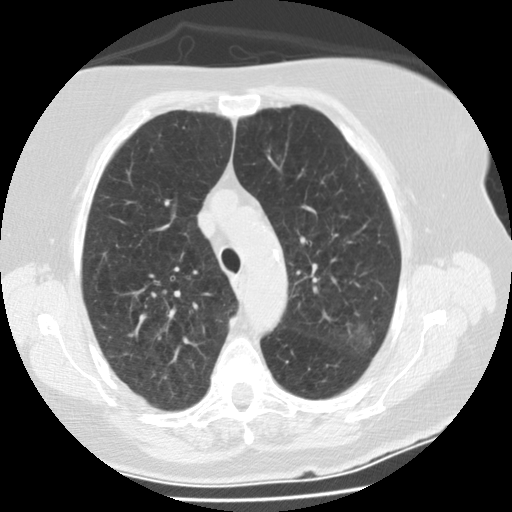
Axial slice from a low-dose chest CT screening exam; second annual screen; lung window (W 1500 / L -600 HU); 2.5 mm slice thickness; 512 × 512 image matrix. Female participant, aged 74 years at enrolment. Former smoker at enrolment.
Expert reader's lesion annotation, box from (x=328, y=311) to (x=386, y=362) px. The screening reader recorded 3 non-calcified nodules or masses ≥4 mm on this exam; which of them this box marks is not recorded. Official screen result: positive, other. Lung cancer was diagnosed 68 days after this screen: bronchiolo-alveolar adenocarcinoma, NOS, left upper lobe, stage IA (AJCC 6th edition), 20 mm at pathology.